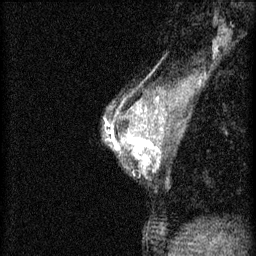
Breast MRI (dynamic contrast-enhanced), one sagittal slice. Position 35 of 46 along the scan axis. 3 images stored at this slice position (order not interpretable as contrast timing). 1.5 T. TE 4.2 ms, TR 8.2 ms. 2 mm slice thickness. 256 × 256 image matrix. Female patient, age 44 years.
Annotated regions visible in this slice (semi-automatically segmented with operator editing):
- analysis volume of interest (the breast-tissue region the enhancement analysis was run in; not a lesion): box from (x=110, y=128) to (x=156, y=175) px
- tumour enhancement mask (voxels above the 70 % enhancement threshold inside the analysis volume of interest): (x=110, y=128)–(x=156, y=169)